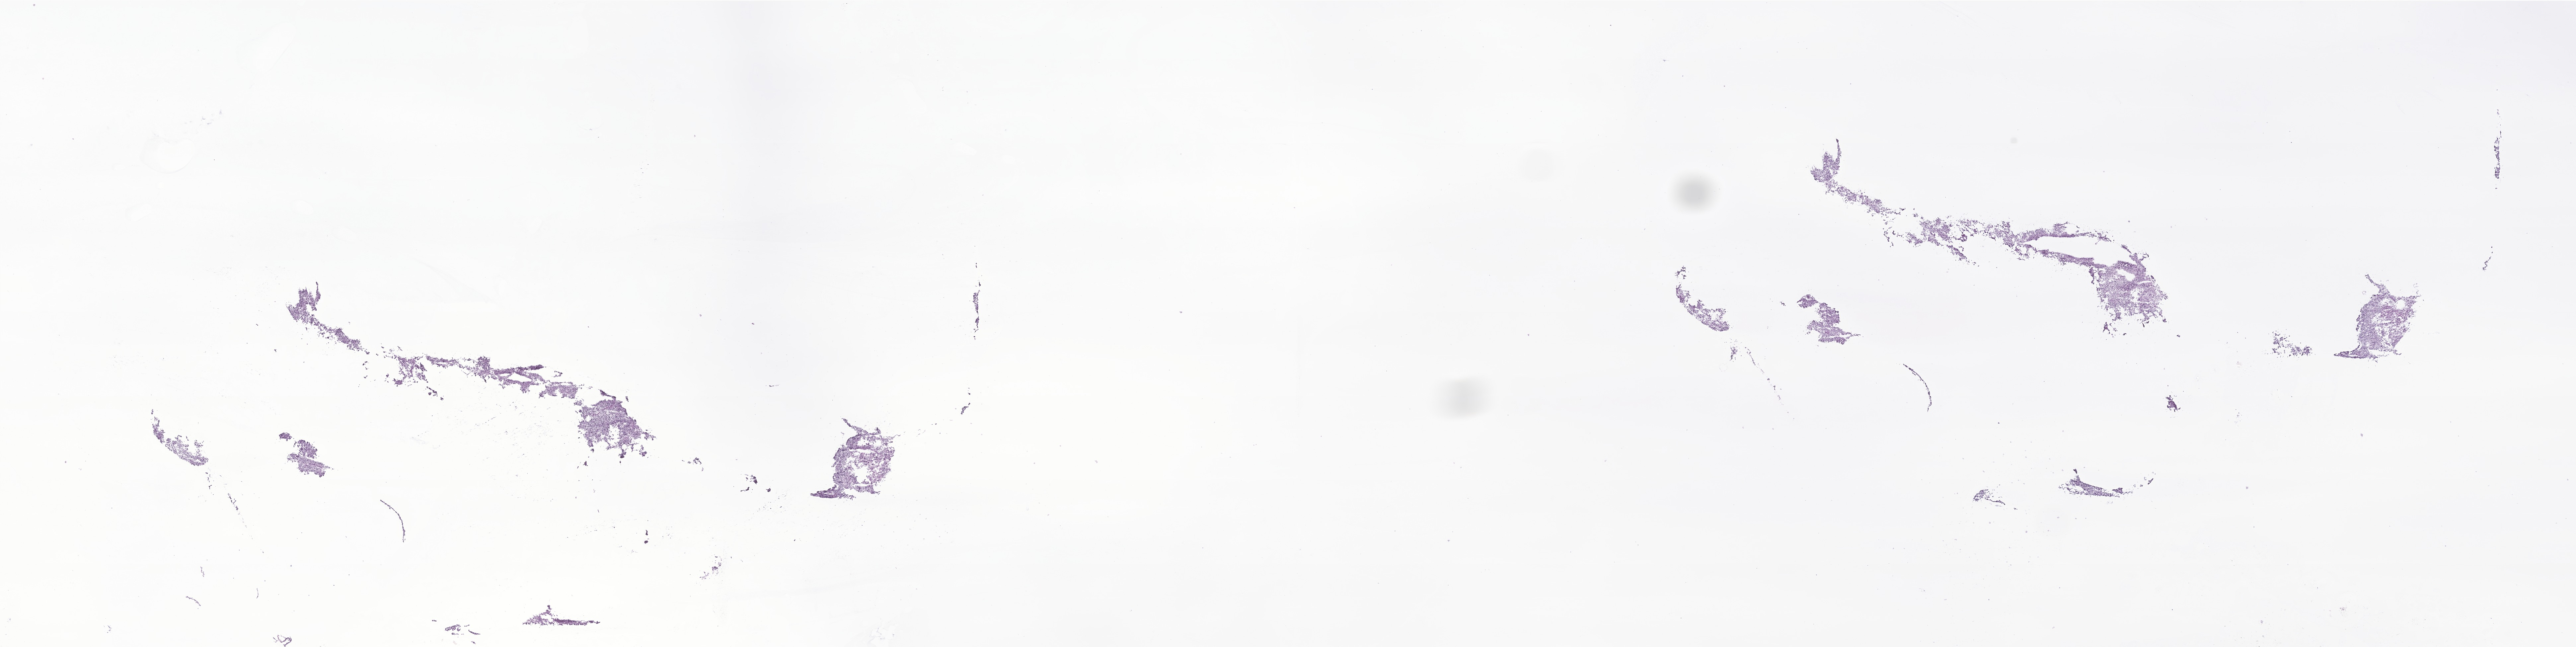
Whole-slide image, H&E stain of tumor tissue from the brain — a low-resolution overview of the entire scanned area, about 32.7 x 8.2 mm; frozen section. Female patient, age 82 months.
Diagnosis (ICD-O-3 morphology term): Glioma, malignant.